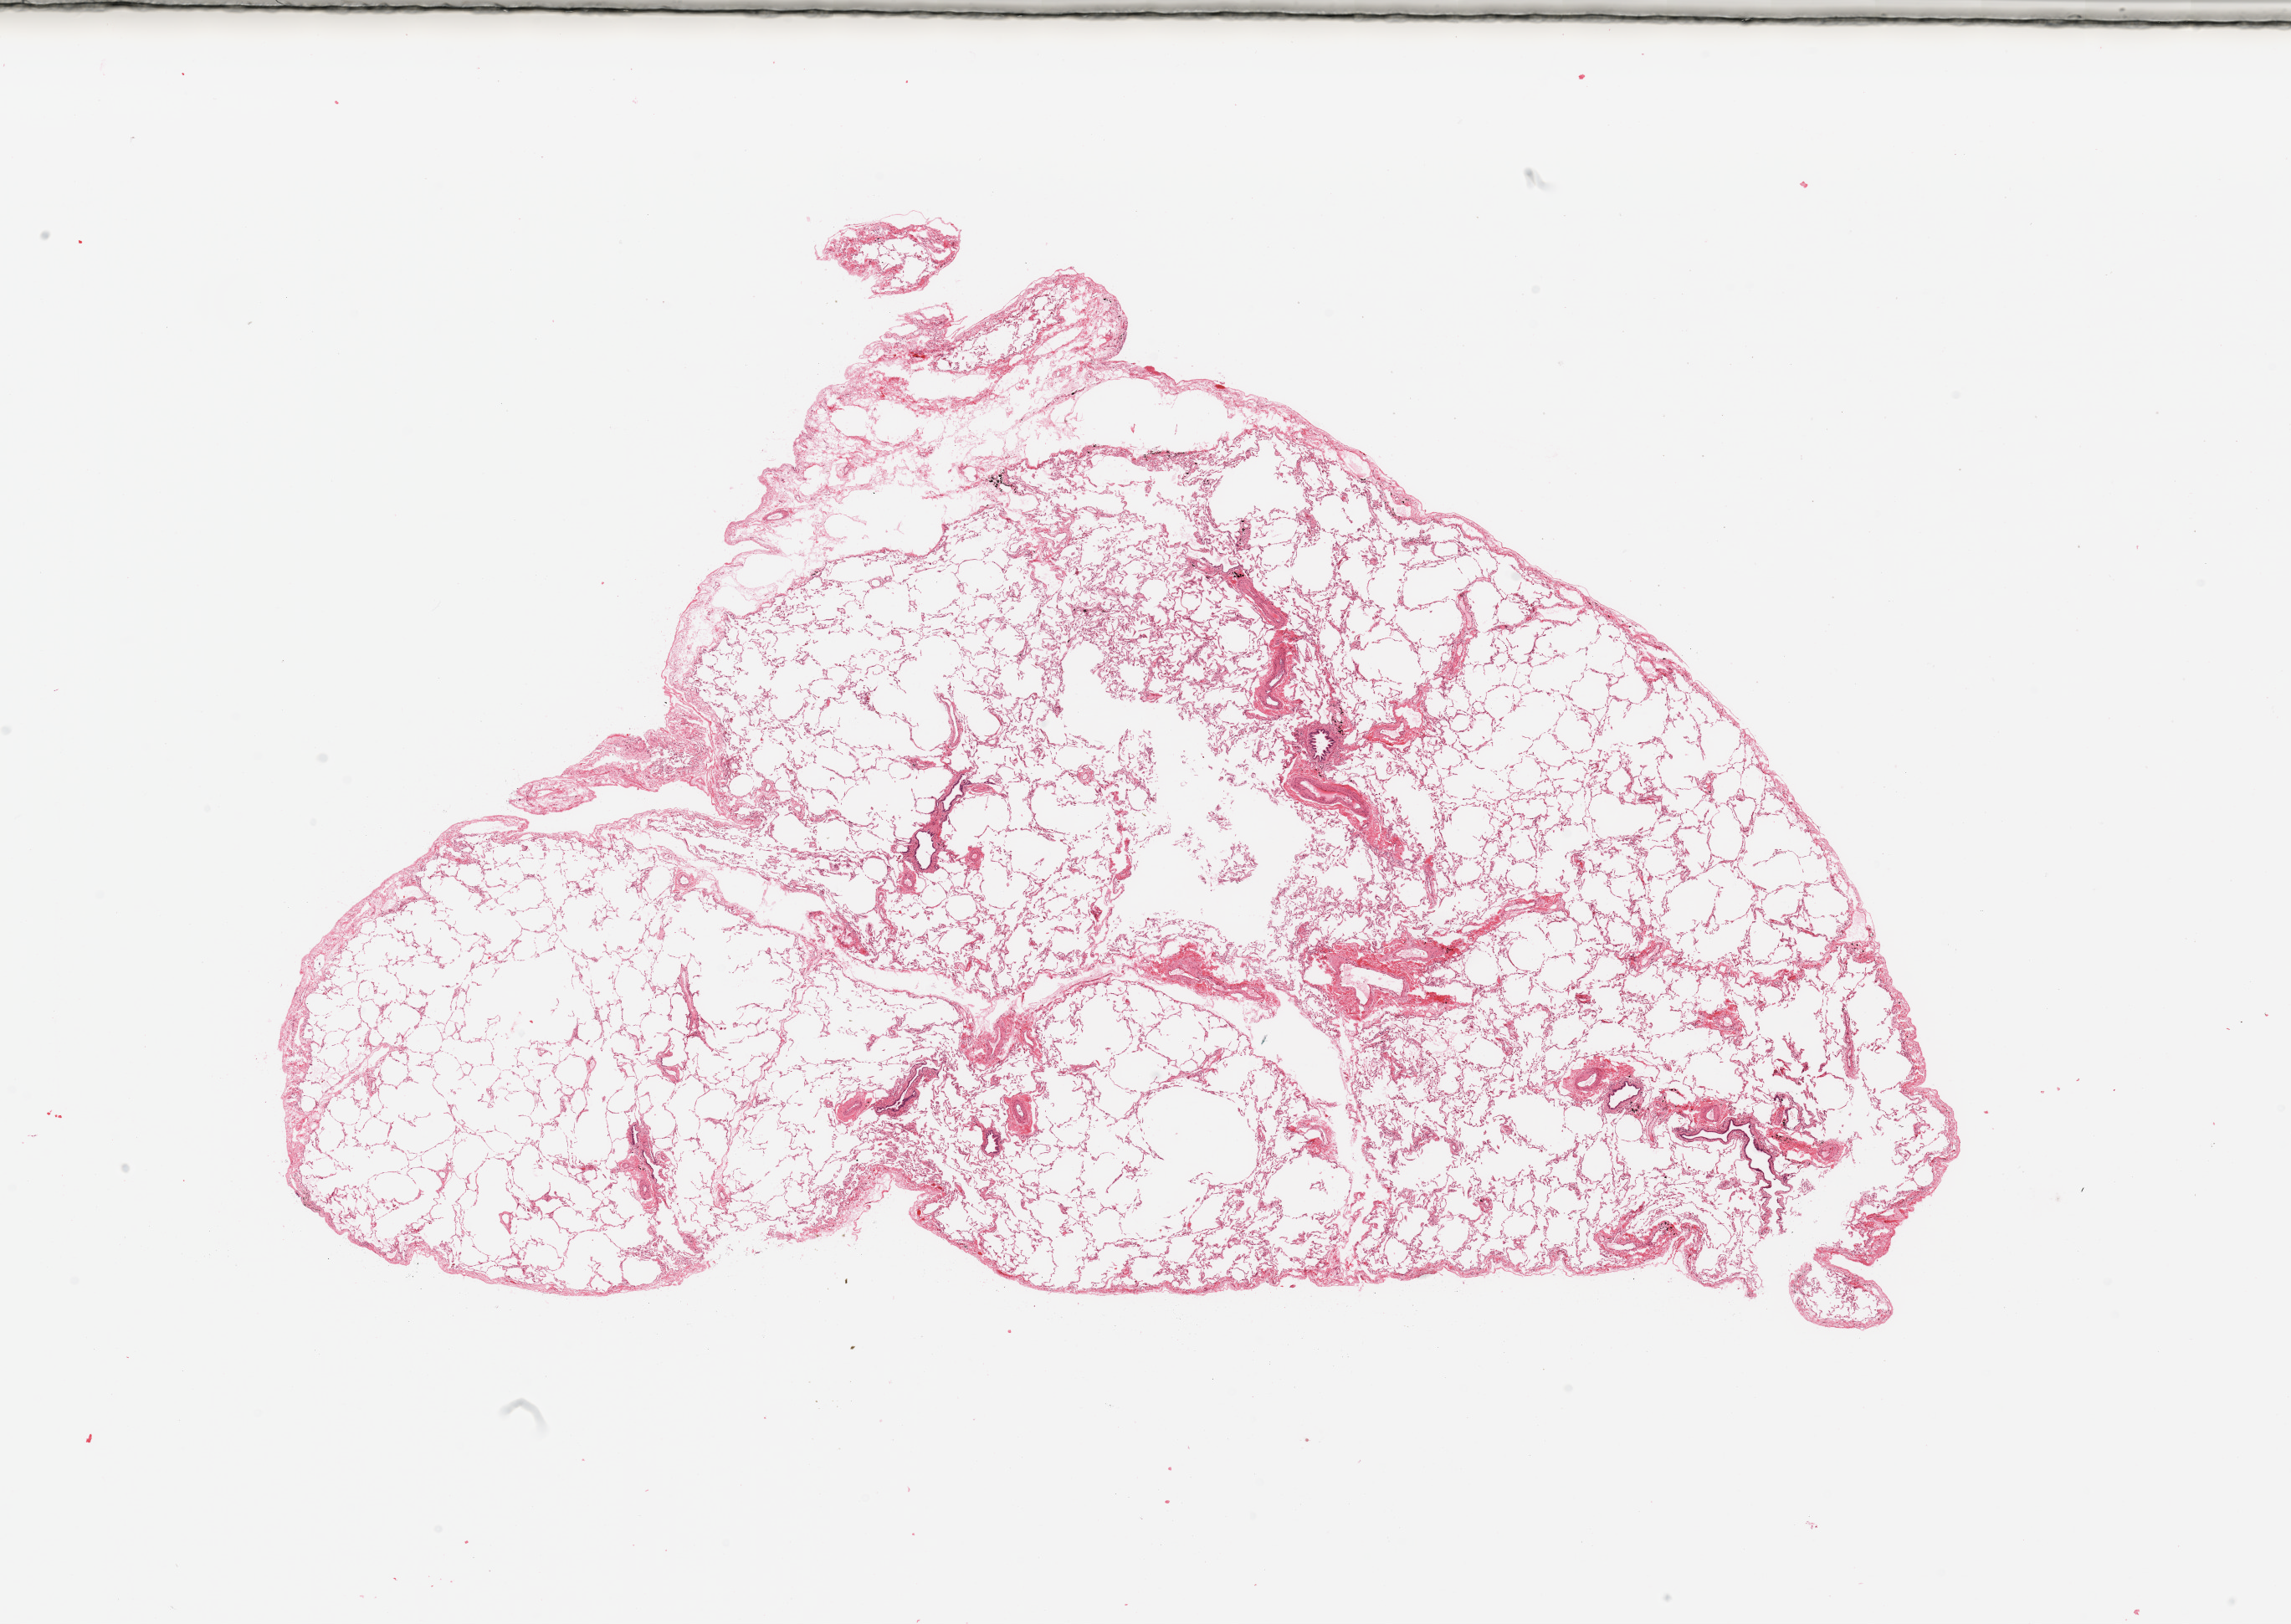
Whole-slide histology image, H&E-stained, shown as a low-resolution overview of the whole scanned area (about 21.7 x 15.4 mm, from a 20x scan). Lung, normal (non-tumour) tissue. Male, 59 y/o.
- this section: normal (non-tumour) tissue from the same patient
- patient diagnosis: Adenocarcinoma, NOS